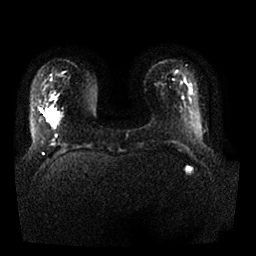
Breast MRI, one axial slice; slice 6 of 25 in the series (ordered by position); diffusion-weighted series; image 2 of 4 stored at this slice position (different b-values; order by instance number); 1.5 T; 4 mm slice thickness; 256 × 256 image matrix, field of view 350 × 350 mm. Female patient.
Annotated regions visible in this slice (expert manual segmentation):
- tumour on diffusion-weighted imaging: bounding box [x1, y1, x2, y2] px = [47, 109, 59, 122]